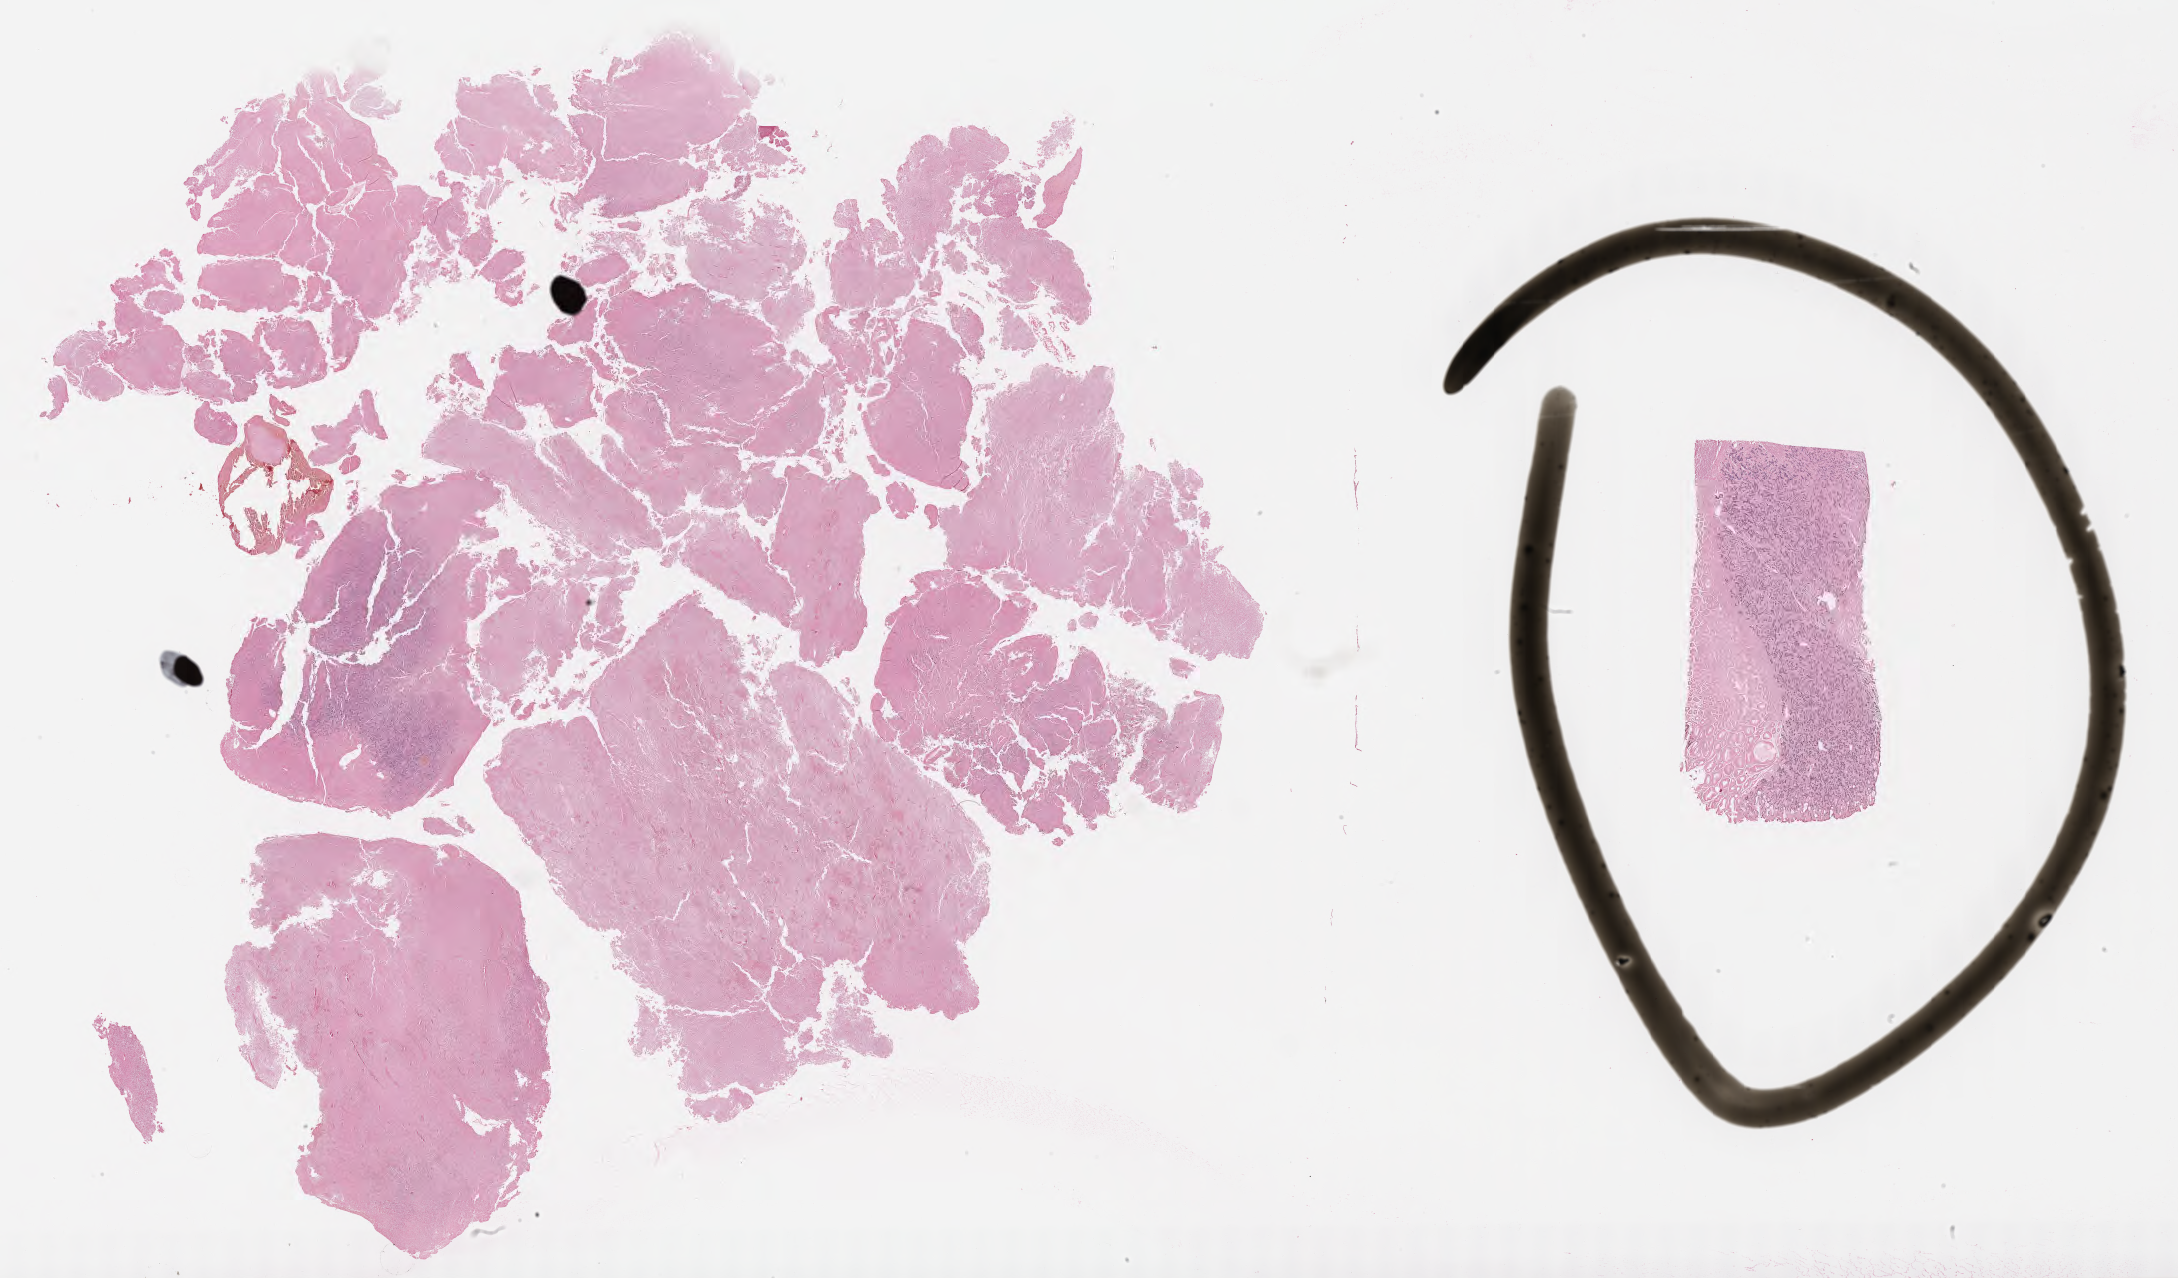
In-situ hybridisation whole-slide image, Epstein–Barr virus-encoded RNA (EBER) probe — whole scanned area (about 35.2 x 20.7 mm) shown as a low-resolution overview, specimen: tumor tissue. Patient: male, 47 years old.
* histologic diagnosis: Diffuse large B-cell lymphoma, NOS